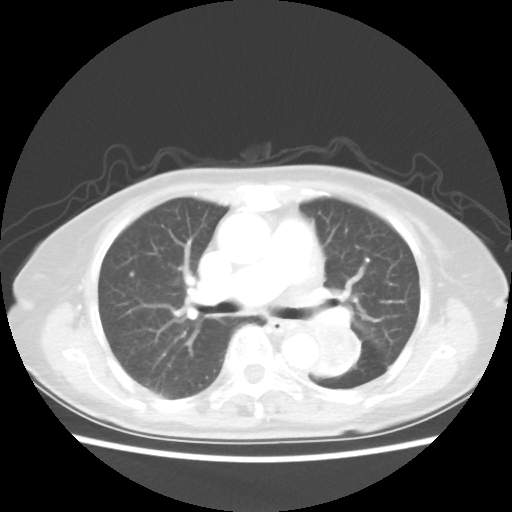
Chest CT, one axial slice; position 30 of 50 along the scan axis; reconstruction kernel STANDARD; 80 kVp; lung window (W 1500 / L -600 HU); 5 mm slice thickness; 512 × 512 image matrix, field of view 335 × 335 mm. Female patient, age 81 years. Case-level facts recorded for this patient, not image findings: clinical TNM (as recorded): T2 N0 M1a.
Outlined on this slice (rectangle marked by the reading radiologist):
- lung tumour (recorded histology: squamous cell carcinoma): bounding box [x1, y1, x2, y2] px = [304, 315, 366, 383]